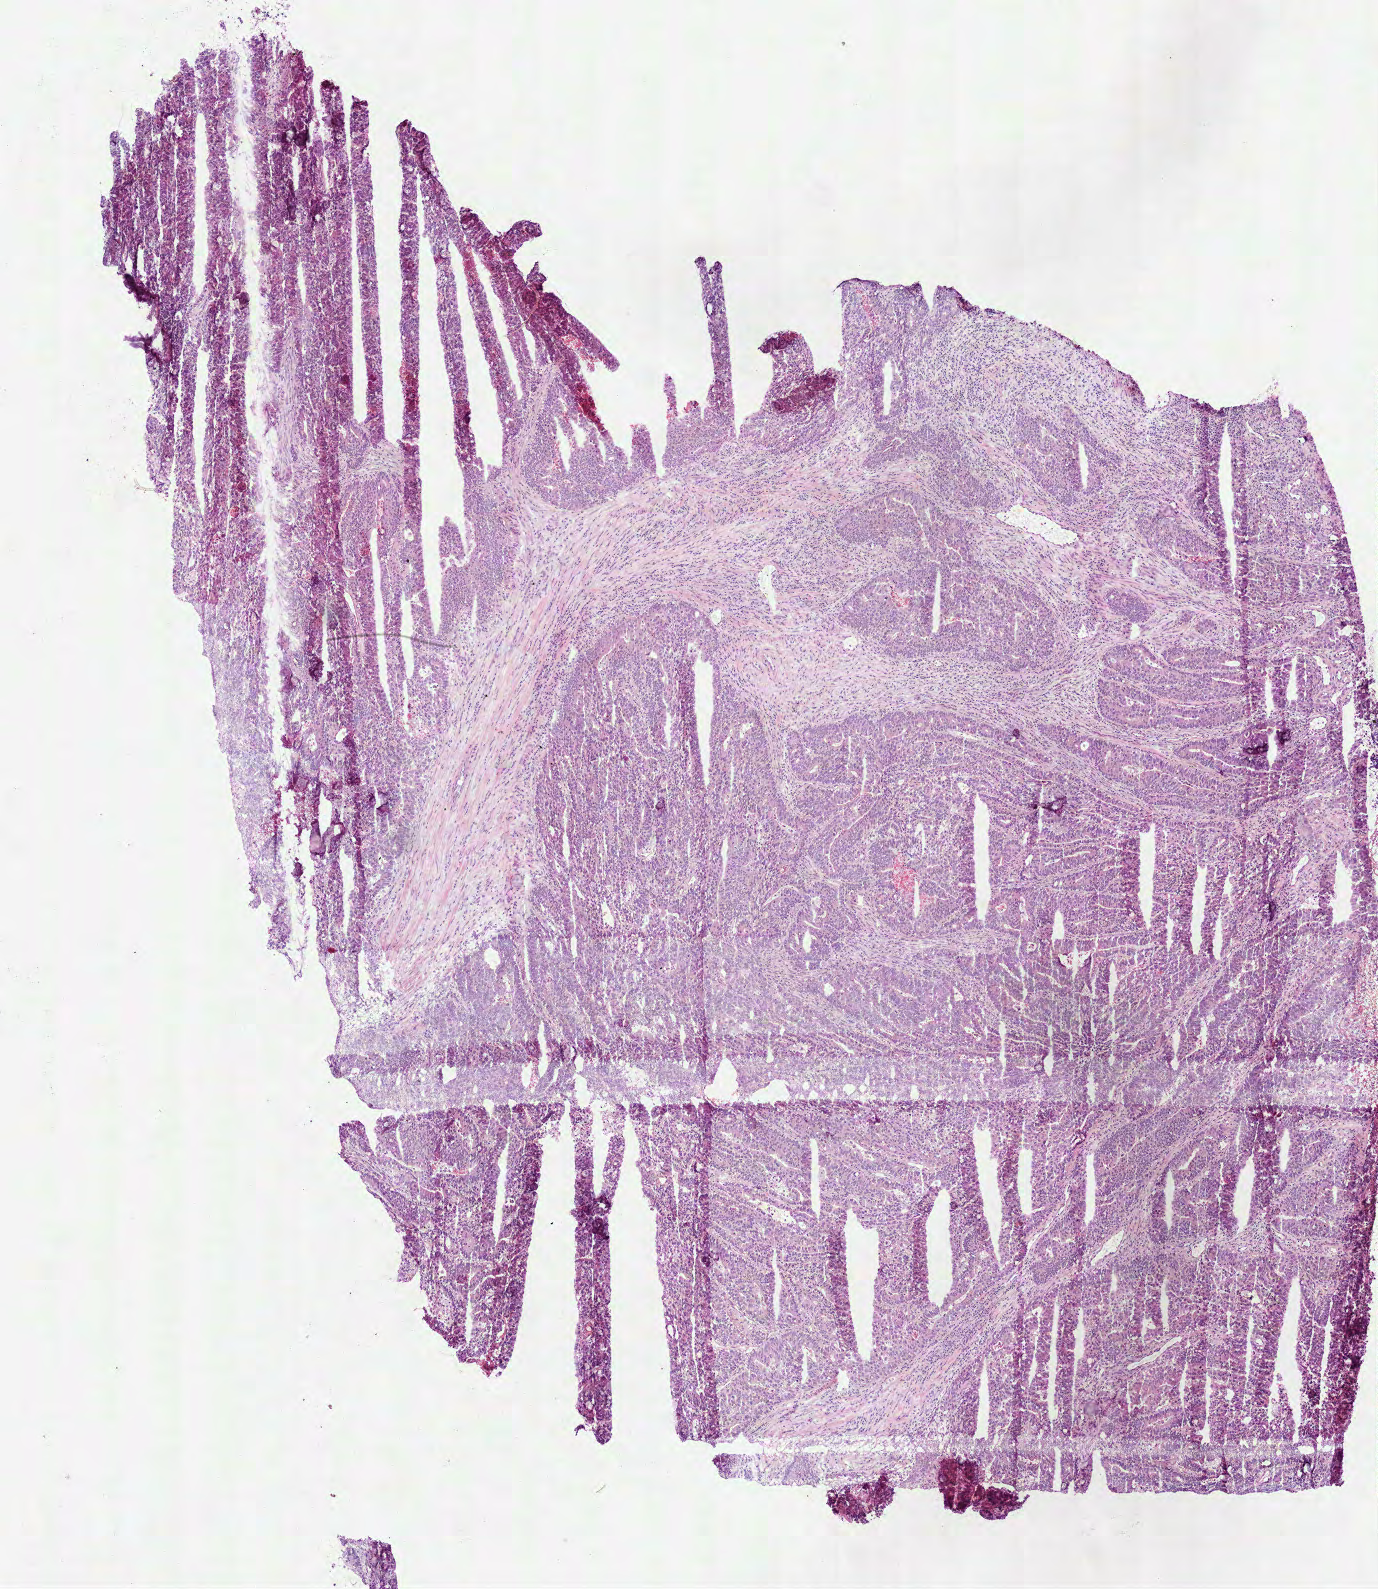
Digitized H&E tissue section (whole slide), a low-resolution overview of the entire scanned area, about 5.6 x 6.4 mm (from a 40x scan). Frozen section from the top of the tissue portion. Primary tumour sample from the rectum. Female, age 57 years at initial diagnosis. Slide review estimates, as recorded: tumour cells 77%, tumour nuclei 75%, normal cells 0%, stromal cells 15%, necrosis 8%.
- AJCC pathologic stage: IV (7th edition)
- pathologic diagnosis: Tubular adenocarcinoma
- lymph nodes positive (case pathology): 2 of 13 examined